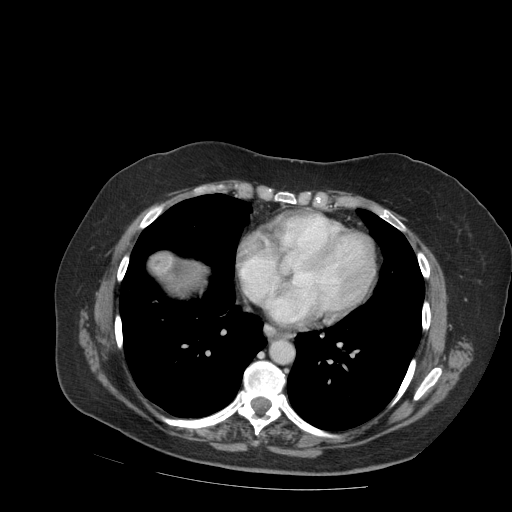
Contrast-enhanced abdominal CT (liver protocol), one axial slice. Slice 91 of 99 in the series (ordered by position). Reconstruction kernel STANDARD. 140 kVp. Soft-tissue window (W 400 / L 40 HU). 2.5 mm slice thickness. 512 × 512 image matrix, field of view 400 × 400 mm. From the clinical record (not read from this slice): diagnosis: hepatocellular carcinoma (patient treated with transarterial chemoembolisation; whether this scan precedes or follows treatment is not stated here); TNM stage (as recorded): Stage-IVB; Child-Pugh class: A; tumour differentiation: moderately differentiated; tumour nodularity: uninodular.
Structures marked on this image (semi-automatic segmentation, software-assisted and operator-edited):
- liver parenchyma outside the tumour (the mass and vessels are separate outlines, so this box may not span the whole liver): box from (x=148, y=250) to (x=206, y=296) px